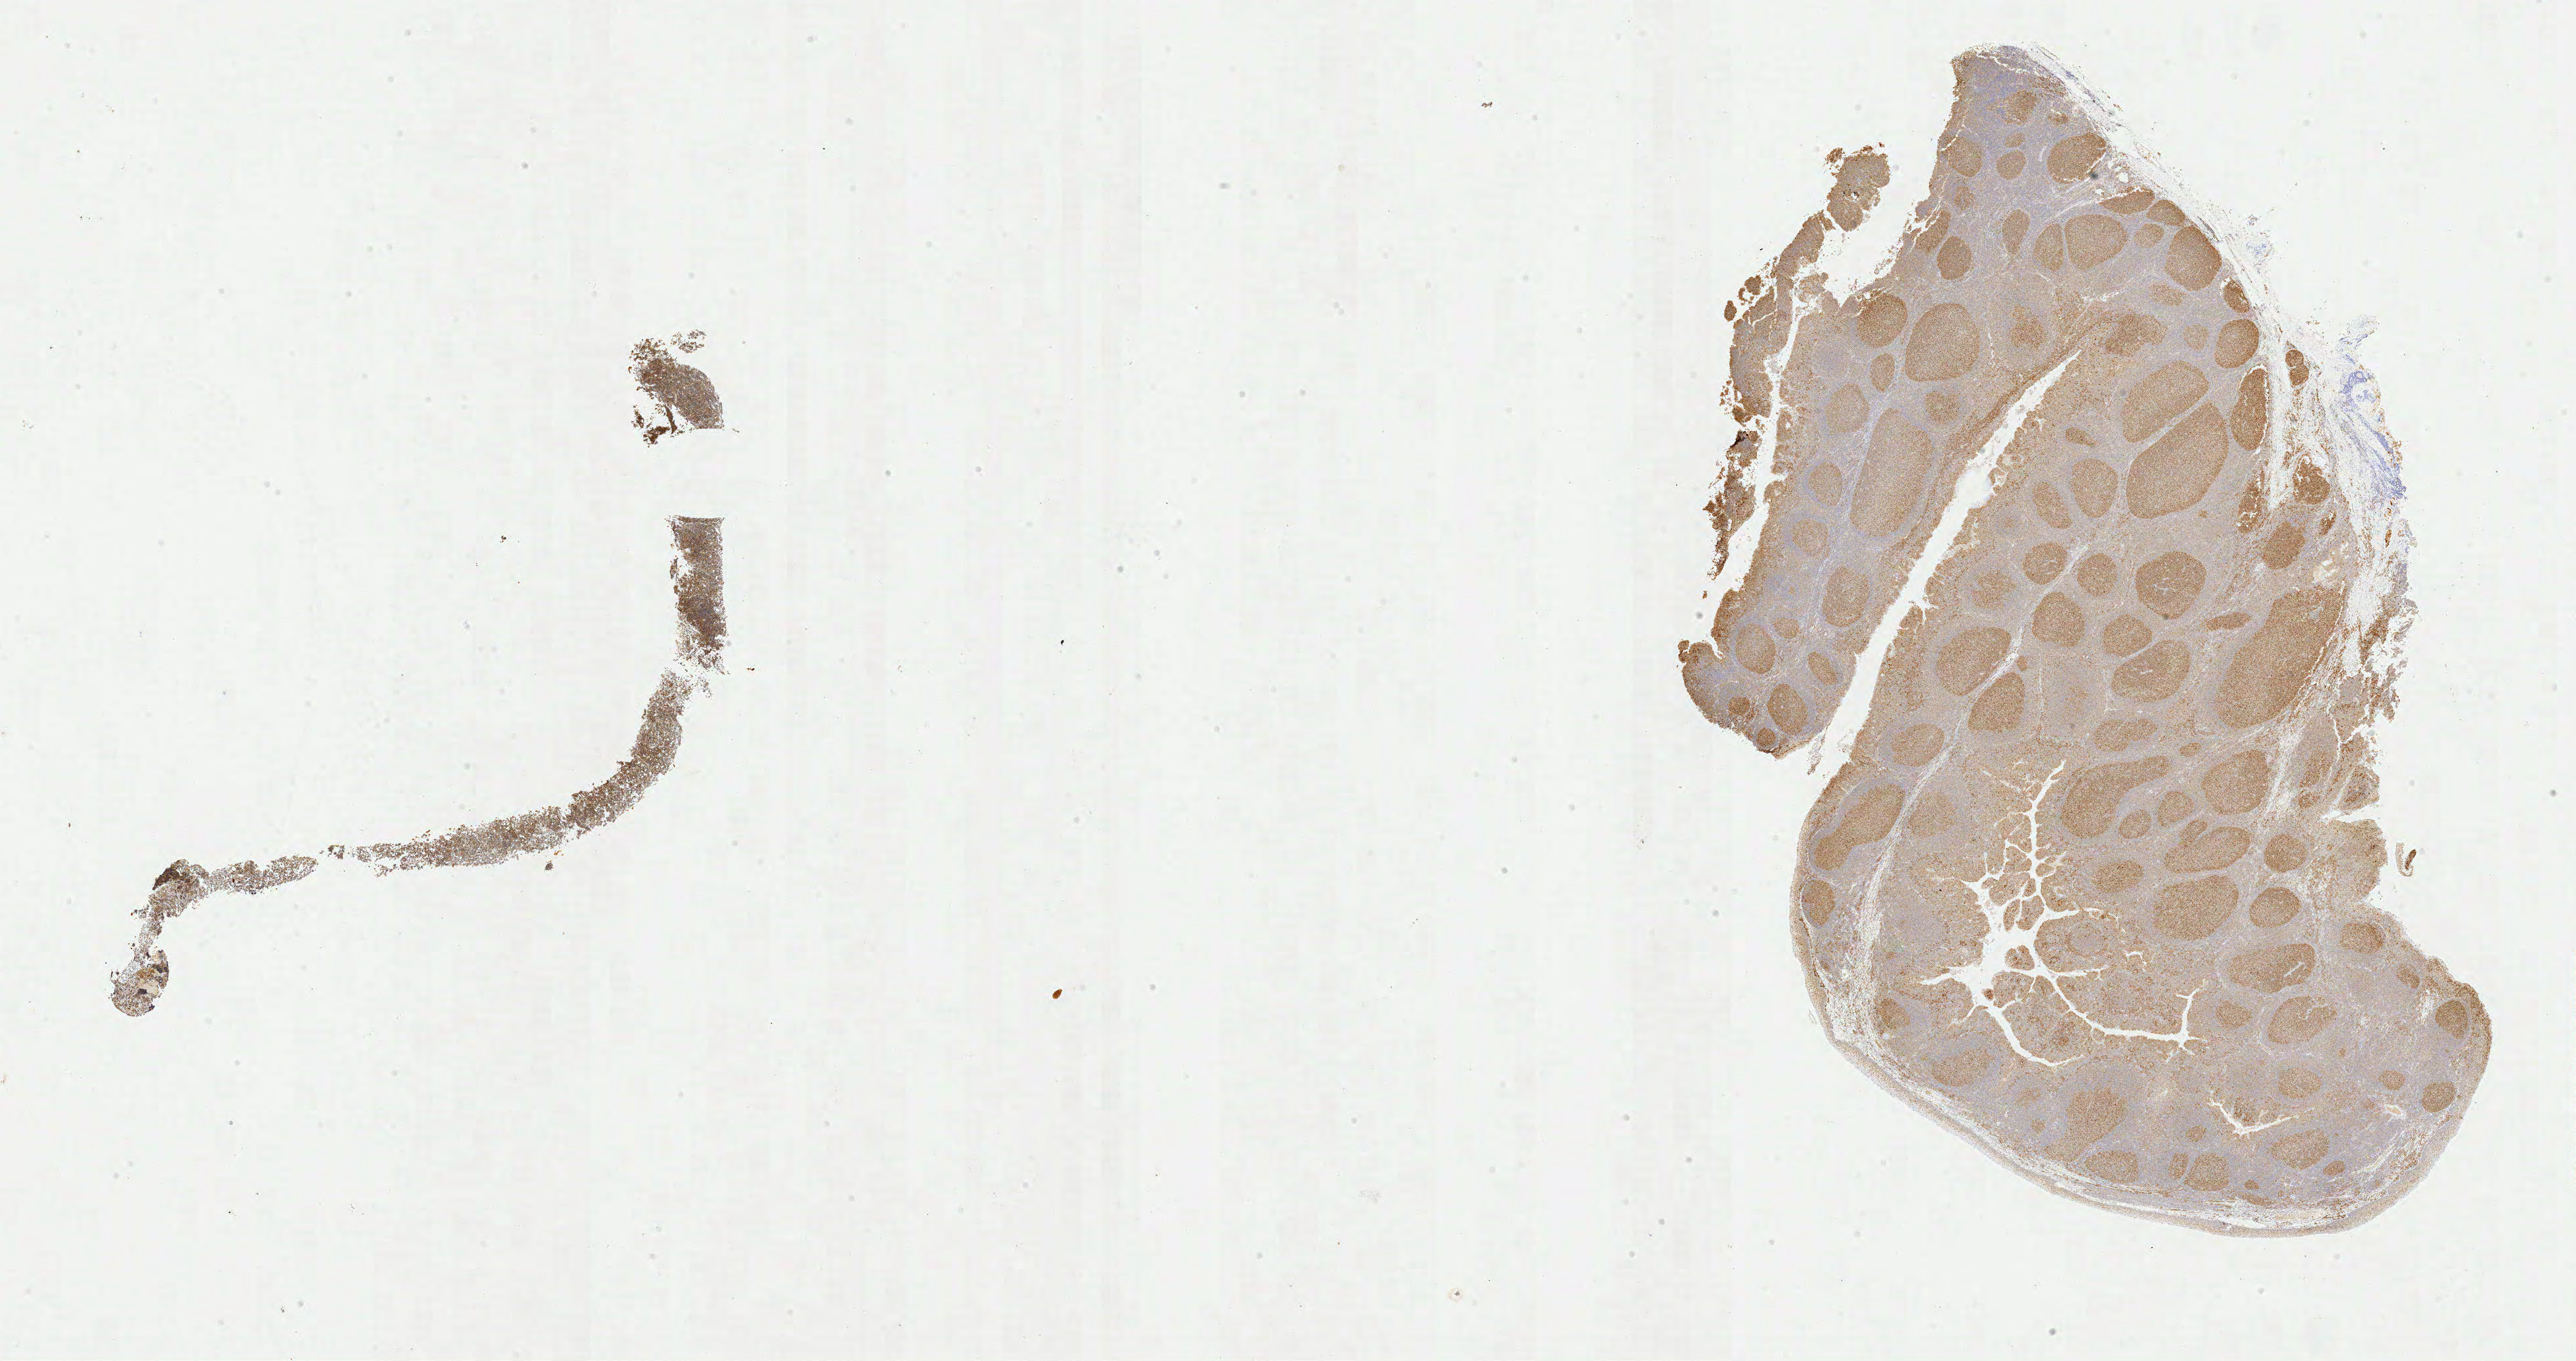
IHC for BCL6, whole-slide image, a low-resolution overview of the entire scanned area, about 30.8 x 16.3 mm; tumor tissue; anatomic site: ovary. Female, age 7 years at initial diagnosis.
Histologic diagnosis: Burkitt lymphoma, NOS.